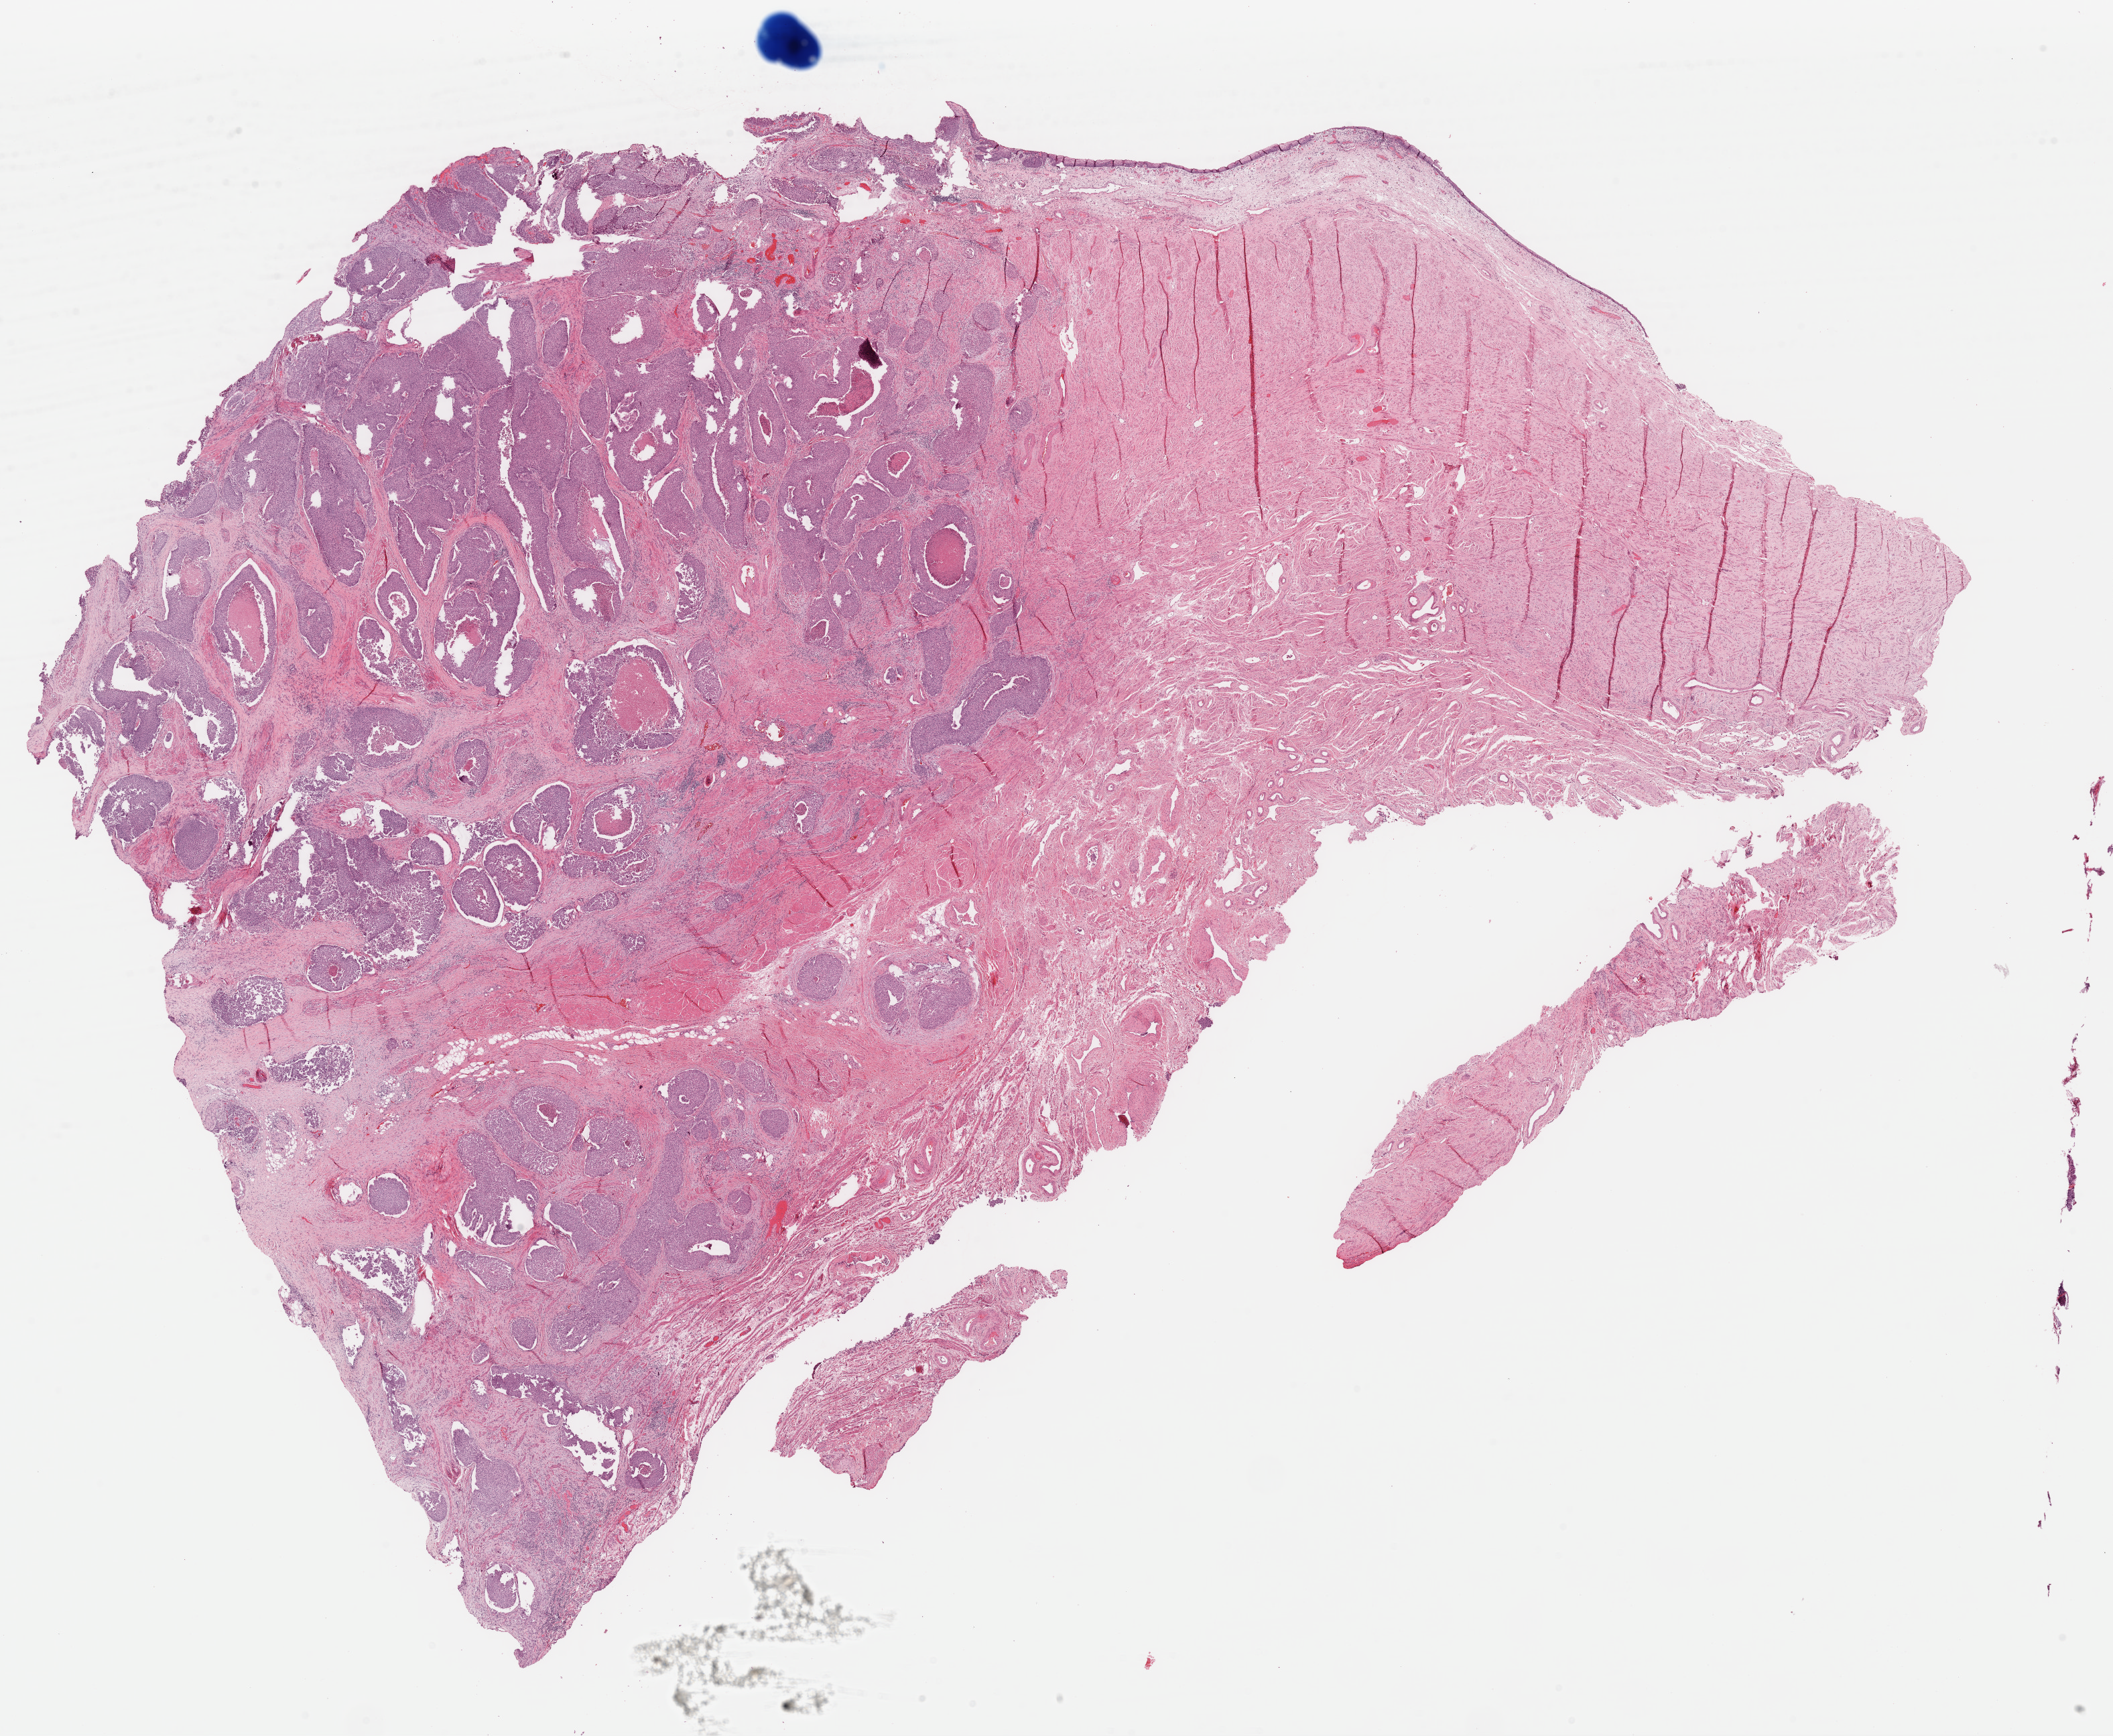
Whole-slide histology image, H&E — shown as a low-resolution overview of the whole scanned area (about 24.9 x 20.5 mm, acquisition: 40x scan); formalin-fixed paraffin-embedded (FFPE) diagnostic section; sample: primary tumour, bladder. Patient: female, age at initial diagnosis 81 years. Histologic grade: high grade.
AJCC pathologic stage: III (6th edition). Pathologic diagnosis: Transitional cell carcinoma (trigone of bladder).